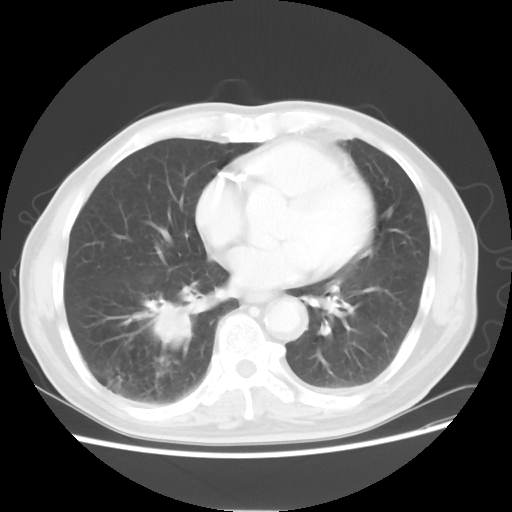
Chest CT, one axial slice. Slice 24 of 58 in the series (ordered by position). Reconstruction kernel STANDARD. 120 kVp. Lung window (W 1500 / L -600 HU). 5 mm slice thickness. 512 × 512 image matrix, field of view 360 × 360 mm. Patient: male, 74 years. From the clinical record (not read from this slice): clinical TNM (as recorded): T1c N1 M1.
Outlined on this slice (bounding box drawn by a radiologist):
- lung tumour (recorded histology: adenocarcinoma): box from (x=117, y=290) to (x=198, y=360) px